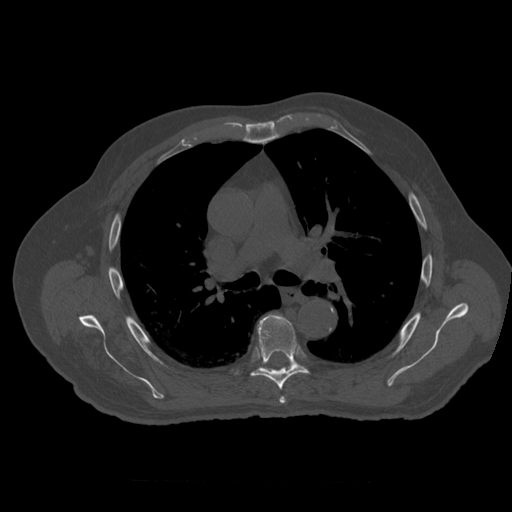
CT including the spine, one axial slice. Slice 383 of 399 in the series (ordered by position). 120 kVp. Bone window (W 1800 / L 400 HU). 512 × 512 image matrix, field of view 407 × 407 mm. Patient age 73 years. Case-level facts recorded for this patient, not image findings: primary cancer: prostate; vertebrae with lytic lesions (as recorded): L2.
Annotated regions visible in this slice (semi-automatically segmented with operator editing):
- T5 vertebra: bounding box [x1, y1, x2, y2] px = [280, 397, 286, 404]
- T6 vertebra: [251, 315, 309, 390]